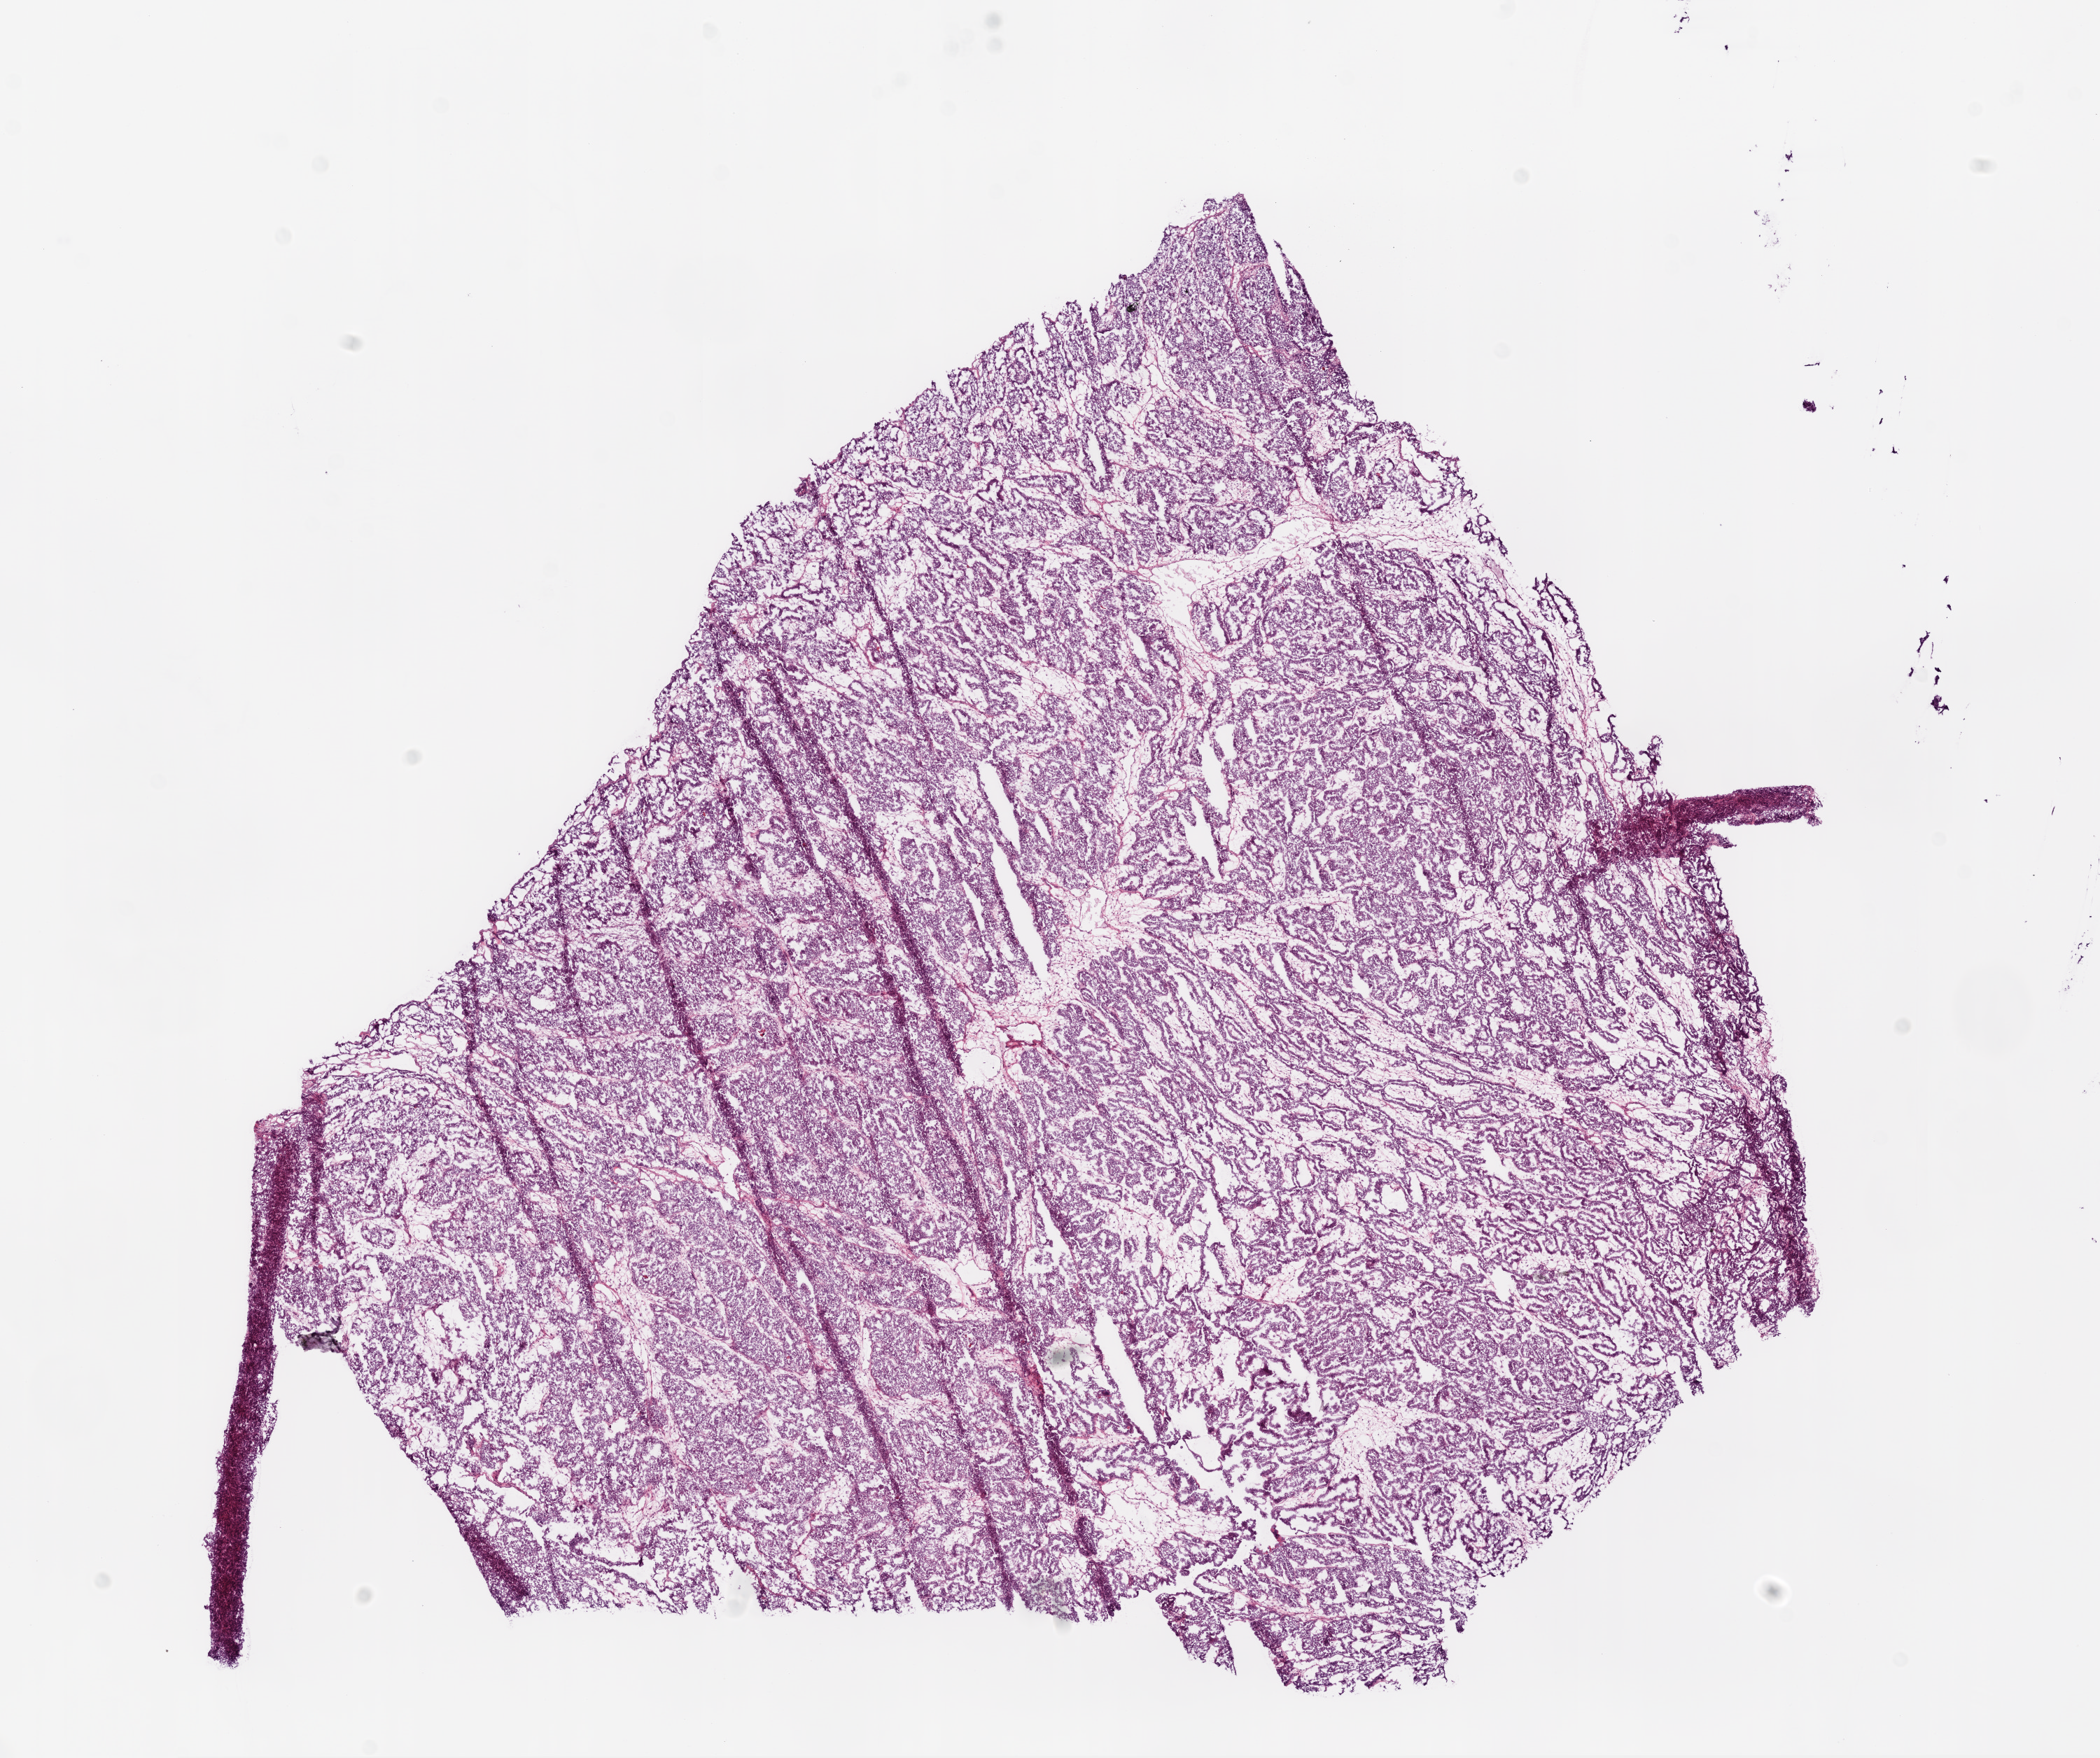
Hematoxylin and eosin (H&E) stained whole-slide image, low-resolution overview of the scanned area, about 12.0 x 10.1 mm (slide scanned at 20x); frozen section from the bottom of the tissue portion; ovary, primary tumour sample. Female, age 50 years at initial diagnosis. Histologic grade: G3 (poorly differentiated). Pathologist review of this section (percent, as recorded): tumour cells 100%, tumour nuclei 90%, normal cells 0%, stromal cells 0%, necrosis 0%. Inflammatory infiltration, as recorded: lymphocyte infiltration 2%, monocyte infiltration 0%, neutrophil infiltration 0%.
Pathologic diagnosis: Serous cystadenocarcinoma, NOS. FIGO stage: IIIA.